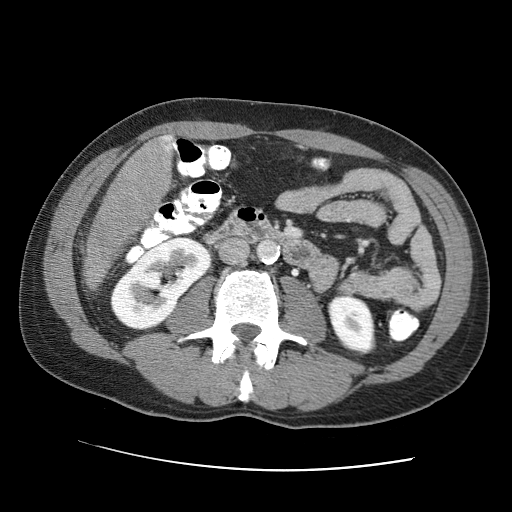
Contrast-enhanced abdominal CT (liver protocol), one axial slice; position 13 of 95 along the scan axis; one of 2 acquisitions stored at this slice position; soft-tissue window (W 400 / L 40 HU); 2.5 mm slice thickness; 512 × 512 image matrix. From the clinical record (not read from this slice): diagnosis: hepatocellular carcinoma (patient treated with transarterial chemoembolisation; whether this scan precedes or follows treatment is not stated here); TNM stage (as recorded): Stage-IVA; Child-Pugh class: A; tumour nodularity: multinodular.
Outlined on this slice (semi-automatically segmented with operator editing):
- liver parenchyma outside the tumour (the mass and vessels are separate outlines, so this box may not span the whole liver): bounding box (x1, y1, x2, y2) in pixels: (84, 134, 175, 277)
- mass: (81, 135, 172, 294)
- liver vessels: (169, 136, 174, 149)